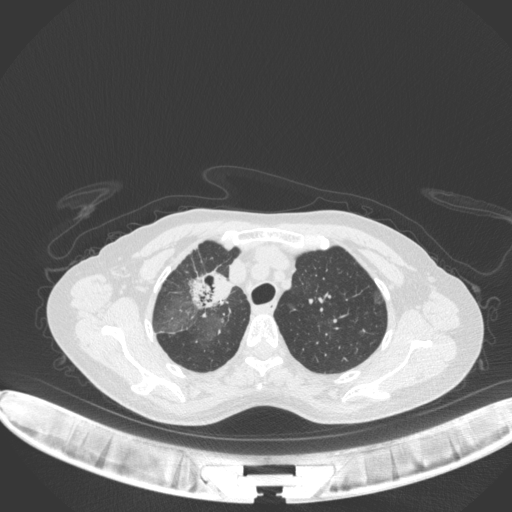
Chest CT, one axial slice; position 255 of 311 along the scan axis; reconstruction kernel B31f; 120 kVp; lung window (W 1500 / L -600 HU); 512 × 512 image matrix, field of view 400 × 400 mm. Female patient, age 59 years. From the clinical record (not read from this slice): clinical TNM (as recorded): T3 N0 M0.
Outlined on this slice (bounding box drawn by a radiologist):
- lung tumour (recorded histology: adenocarcinoma): bounding box [x1, y1, x2, y2] px = [189, 258, 235, 317]